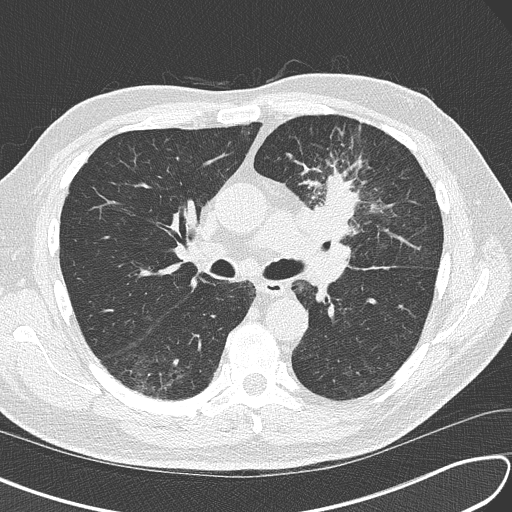
Axial slice from a low-dose chest CT screening exam. Third screening round (two years after baseline). Lung window (W 1500 / L -600 HU). 2 mm slice thickness. Lung (sharp) reconstruction kernel (B50f). Slice 63 of 156 in the series. Male participant, aged 67 years at enrolment. Current smoker at enrolment.
Expert-annotated lung lesion, bounding box (x1, y1, x2, y2) in pixels: (295, 163, 395, 254). Reader record for this screening exam (exam-level; its link to the box is not recorded): non-calcified nodule or mass ≥4 mm, left upper lobe, 30 × 23 mm, soft tissue attenuation, pre-existing on the prior screen: no. Official screen result: positive, other. Participant outcome: lung cancer diagnosed 41 days after this screen — small cell carcinoma, NOS, left upper lobe, stage IV (AJCC 6th edition), 30 mm at pathology.